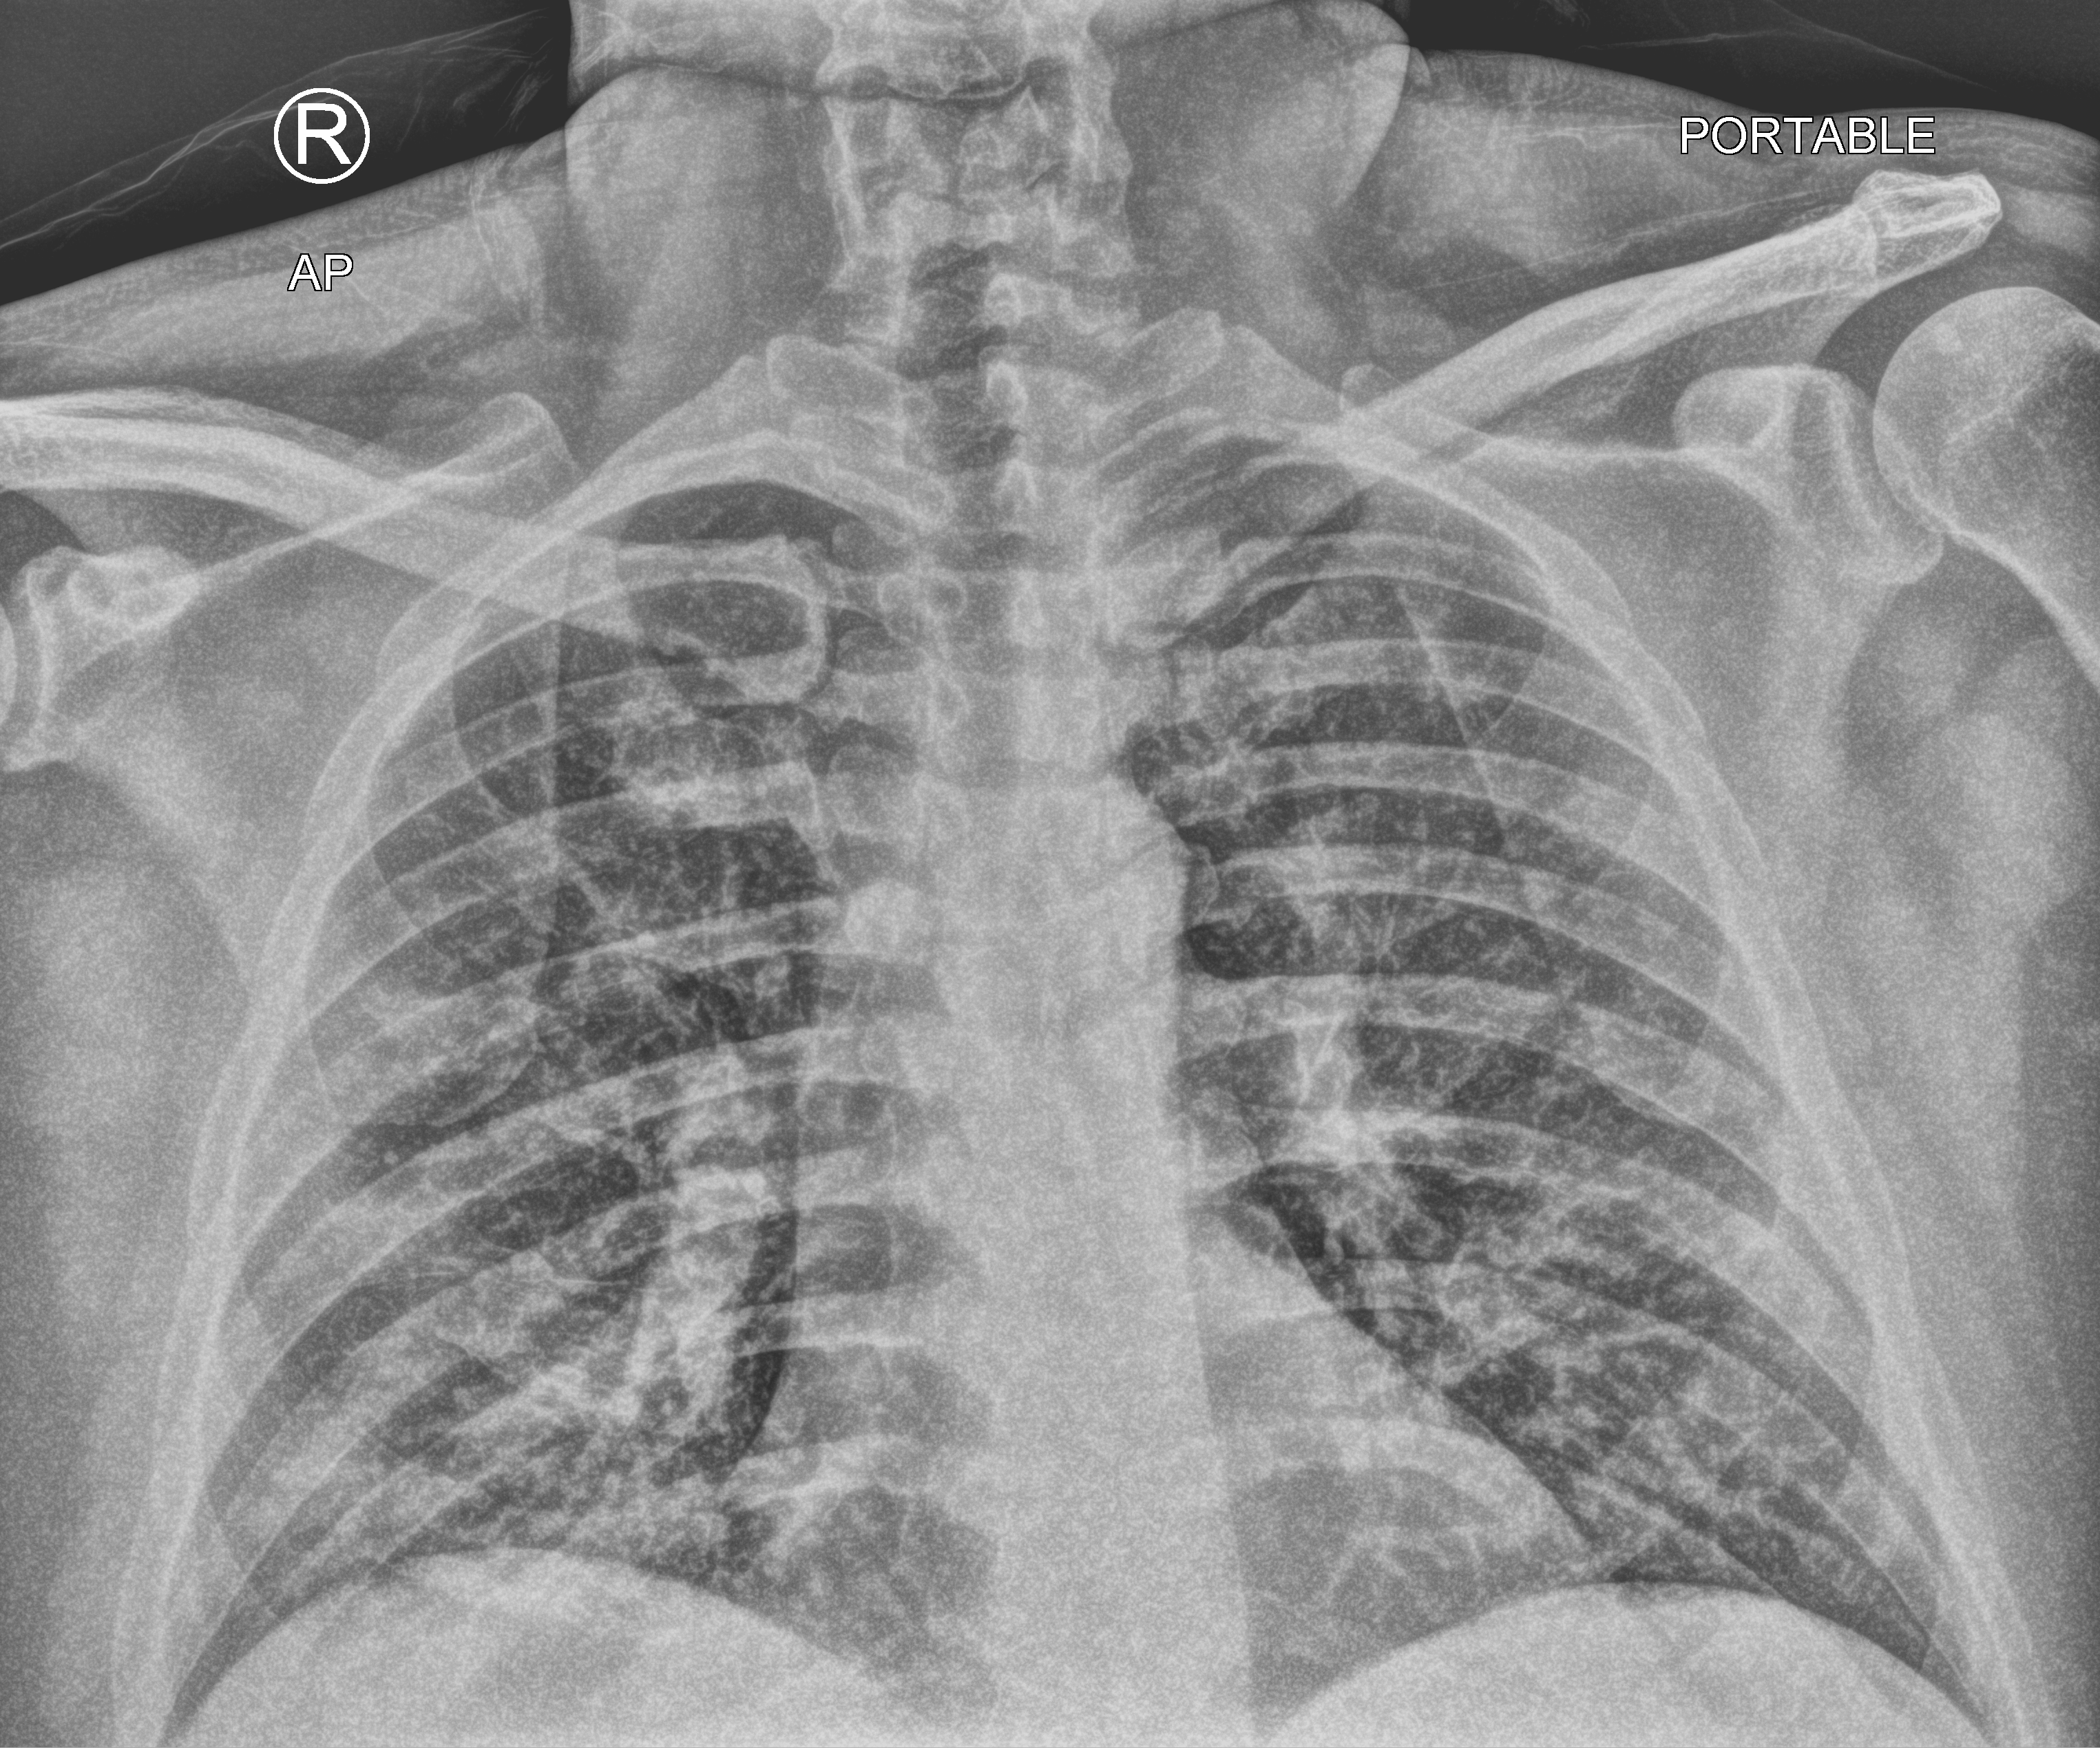
Chest X-ray (portable). Male patient hospitalised with COVID-19, age 18–59 years.
Admission-level facts for this patient (not findings on this image; timing relative to this image not recorded): admitted to intensive care during this hospital stay: no.